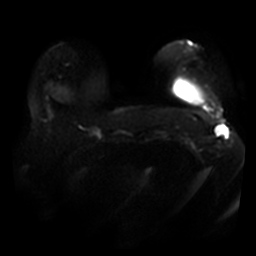
Breast MRI, one axial slice. Slice 7 of 40 in the series (ordered by position). Diffusion-weighted series; image 2 of 4 stored at this slice position (different b-values; order by instance number). 3 T. 5 mm slice thickness. 256 × 256 image matrix. Female patient.
Structures marked on this image (manually delineated by an expert):
- tumour on diffusion-weighted imaging: box from (x=223, y=128) to (x=228, y=134) px